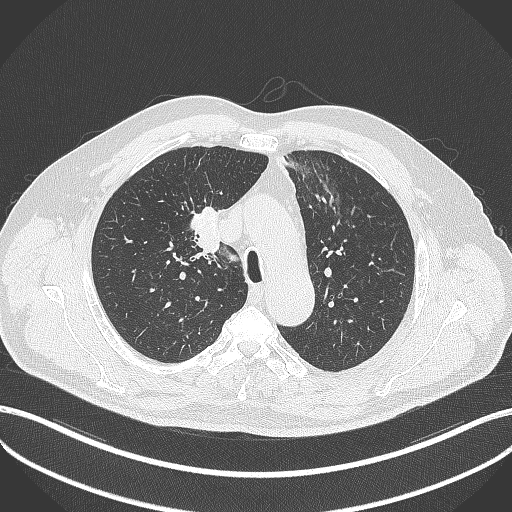
Chest CT, one axial slice. Position 283 of 411 along the scan axis. Reconstruction kernel B70f. 120 kVp. Lung window (W 1500 / L -600 HU). 1 mm slice thickness. 512 × 512 image matrix. Male patient, age 60 years. From the clinical record (not read from this slice): clinical TNM (as recorded): T1b N1 M0.
Outlined on this slice (bounding box drawn by a radiologist):
- lung tumour (recorded histology: squamous cell carcinoma): bounding box (x1, y1, x2, y2) in pixels: (187, 200, 222, 261)